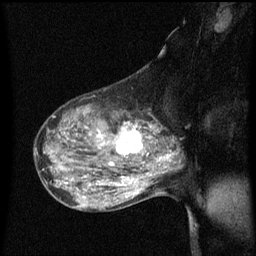
Breast MRI (dynamic contrast-enhanced), one sagittal slice; slice 38 of 60 in the series (ordered by position); dynamic contrast-enhanced series, image 2 of 3 at this slice position (ordered by acquisition); 1.5 T; TE 4.2 ms, TR 8.4 ms; 2 mm slice thickness; 256 × 256 image matrix, field of view 200 × 200 mm. Patient: female, 50 years.
Annotated regions visible in this slice (semi-automatic segmentation, software-assisted and operator-edited):
- analysis volume of interest (the breast-tissue region the enhancement analysis was run in; not a lesion): bounding box (x1, y1, x2, y2) in pixels: (100, 114, 153, 171)
- tumour enhancement mask (voxels above the 70 % enhancement threshold inside the analysis volume of interest): (100, 122, 152, 165)